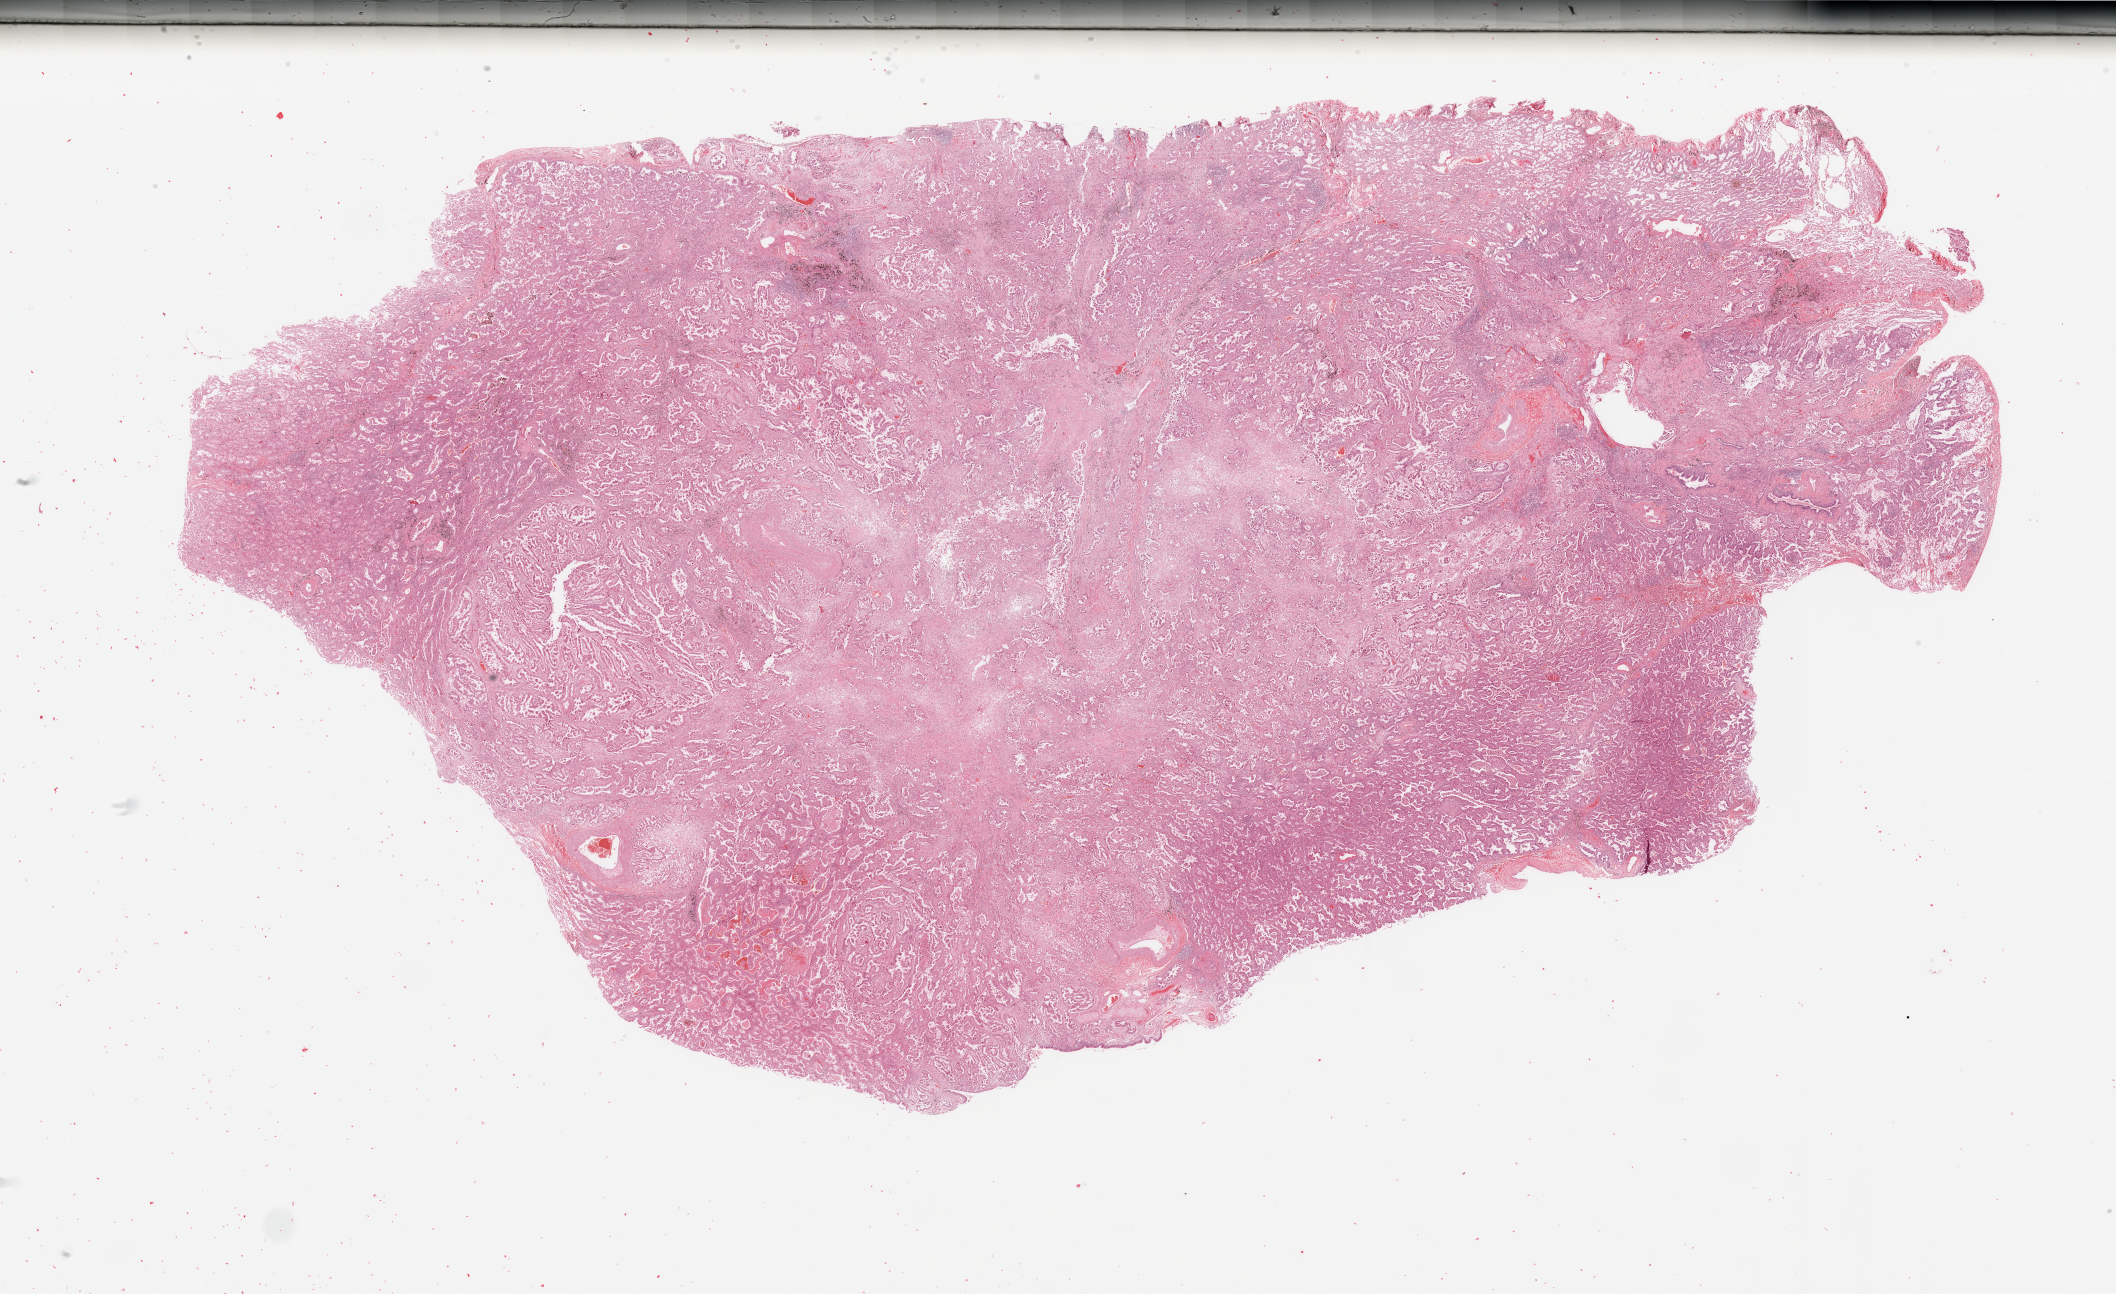
Digitized H&E-stained tissue section (whole slide) — shown as a low-resolution overview of the whole scanned area (about 33.5 x 20.5 mm, slide scanned at 20x). Lung, tumour tissue. Patient: male, age 64 years.
Histologic diagnosis: Adenocarcinoma, NOS.